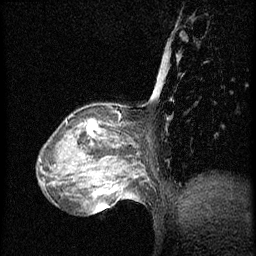
Breast MRI (dynamic contrast-enhanced), one sagittal slice. Slice 18 of 56 in the series (ordered by position). Dynamic contrast-enhanced series, image 2 of 3 at this slice position (ordered by acquisition). 1.5 T. TE 4.2 ms, TR 20.4 ms. 2 mm slice thickness. 256 × 256 image matrix, field of view 200 × 200 mm. Patient: female, 64 years. From the clinical record (not read from this slice): setting: breast cancer imaged before/during neoadjuvant chemotherapy; receptor status: HR-positive, HER2-negative.
Structures marked on this image (semi-automatic segmentation, software-assisted and operator-edited):
- analysis volume of interest (the breast-tissue region the enhancement analysis was run in; not a lesion): bounding box (x1, y1, x2, y2) in pixels: (48, 104, 142, 186)
- tumour enhancement mask (voxels above the 70 % enhancement threshold inside the analysis volume of interest): (87, 119, 101, 133)